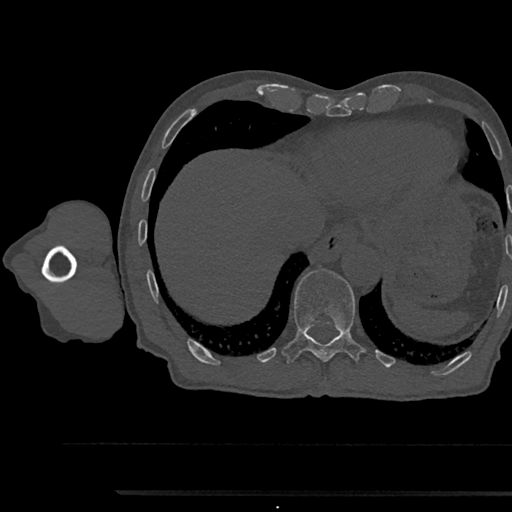
CT including the spine, one axial slice. Slice 791 of 797 in the series (ordered by position). Reconstruction kernel Br40s/3. 120 kVp. Bone window (W 1800 / L 400 HU). 0.5 mm slice thickness. 512 × 512 image matrix, field of view 367 × 367 mm. Patient: male, 79 years. From the clinical record (not read from this slice): primary cancer: prostate.
Outlined on this slice (semi-automatically segmented with operator editing):
- T11 vertebra: bounding box <282,269,365,363> (left, top, right, bottom; pixels)